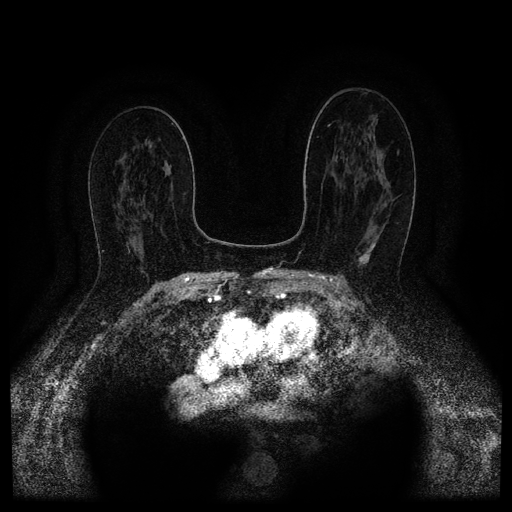
Breast MRI (dynamic contrast-enhanced, multi-phase), one axial slice. Slice 62 of 116 in the series (ordered by position). Dynamic contrast-enhanced series, time point 2 of 5 at this slice position (early post-contrast). 1.5 T. TE 2.6 ms, TR 5.4 ms. 512 × 512 image matrix, field of view 340 × 340 mm. Female patient, age 67 years.
Annotated regions visible in this slice (semi-automatic segmentation, software-assisted and operator-edited):
- breast lesion (labelled 'tumour' in the annotation; benign lesions carry a separate 'benign' label): bounding box (x1, y1, x2, y2) in pixels: (359, 231, 382, 267)